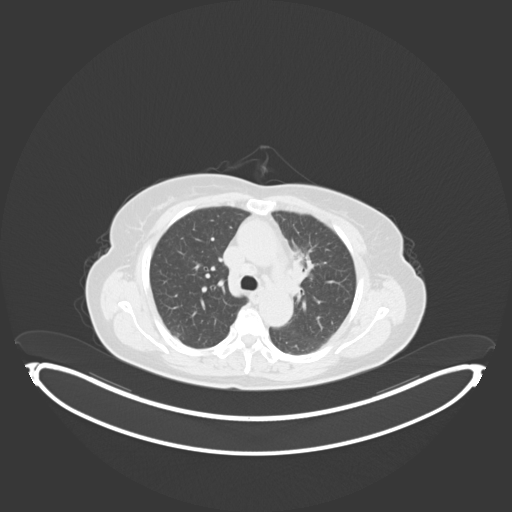
Chest CT, one axial slice; reconstruction kernel B30f; 120 kVp; lung window (W 1500 / L -600 HU); 3 mm slice thickness; 512 × 512 image matrix, field of view 500 × 500 mm. Patient: female, 65 years. Case-level facts recorded for this patient, not image findings: clinical TNM (as recorded): T2a N0 M0; histopathological grade: G2-3.
Structures marked on this image (bounding box drawn by a radiologist):
- lung tumour (recorded histology: adenocarcinoma): bounding box <291,244,314,286> (left, top, right, bottom; pixels)